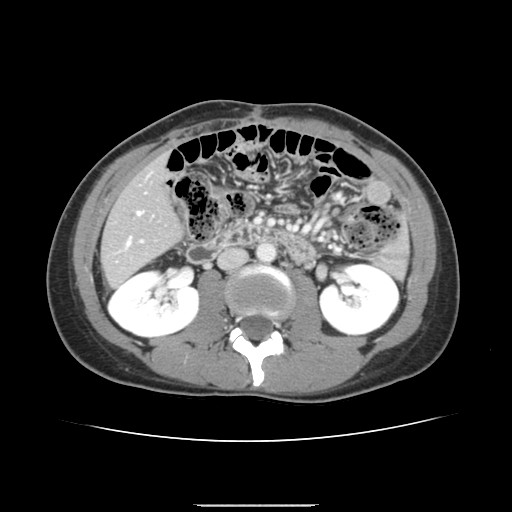
Contrast-enhanced abdominal CT, one axial slice; slice 55 of 150 in the series (ordered by position); 120 kVp; intravenous contrast given; soft-tissue window (W 400 / L 40 HU); 2.5 mm slice thickness; 512 × 512 image matrix. Female patient, age 32 years. Case-level facts recorded for this patient, not image findings: diagnosis: colorectal cancer liver metastases, imaged before liver resection; multiple liver metastases: yes; largest metastasis: 0.7 cm; disease in both lobes: no.
Annotated regions visible in this slice (manually delineated by an expert):
- hepatic veins: bounding box [x1, y1, x2, y2] px = [126, 211, 142, 247]
- liver: [102, 158, 181, 286]
- planned liver remnant (the part of the liver to remain after resection): [102, 158, 181, 286]
- portal vein (with intrahepatic branches): [140, 240, 143, 242]